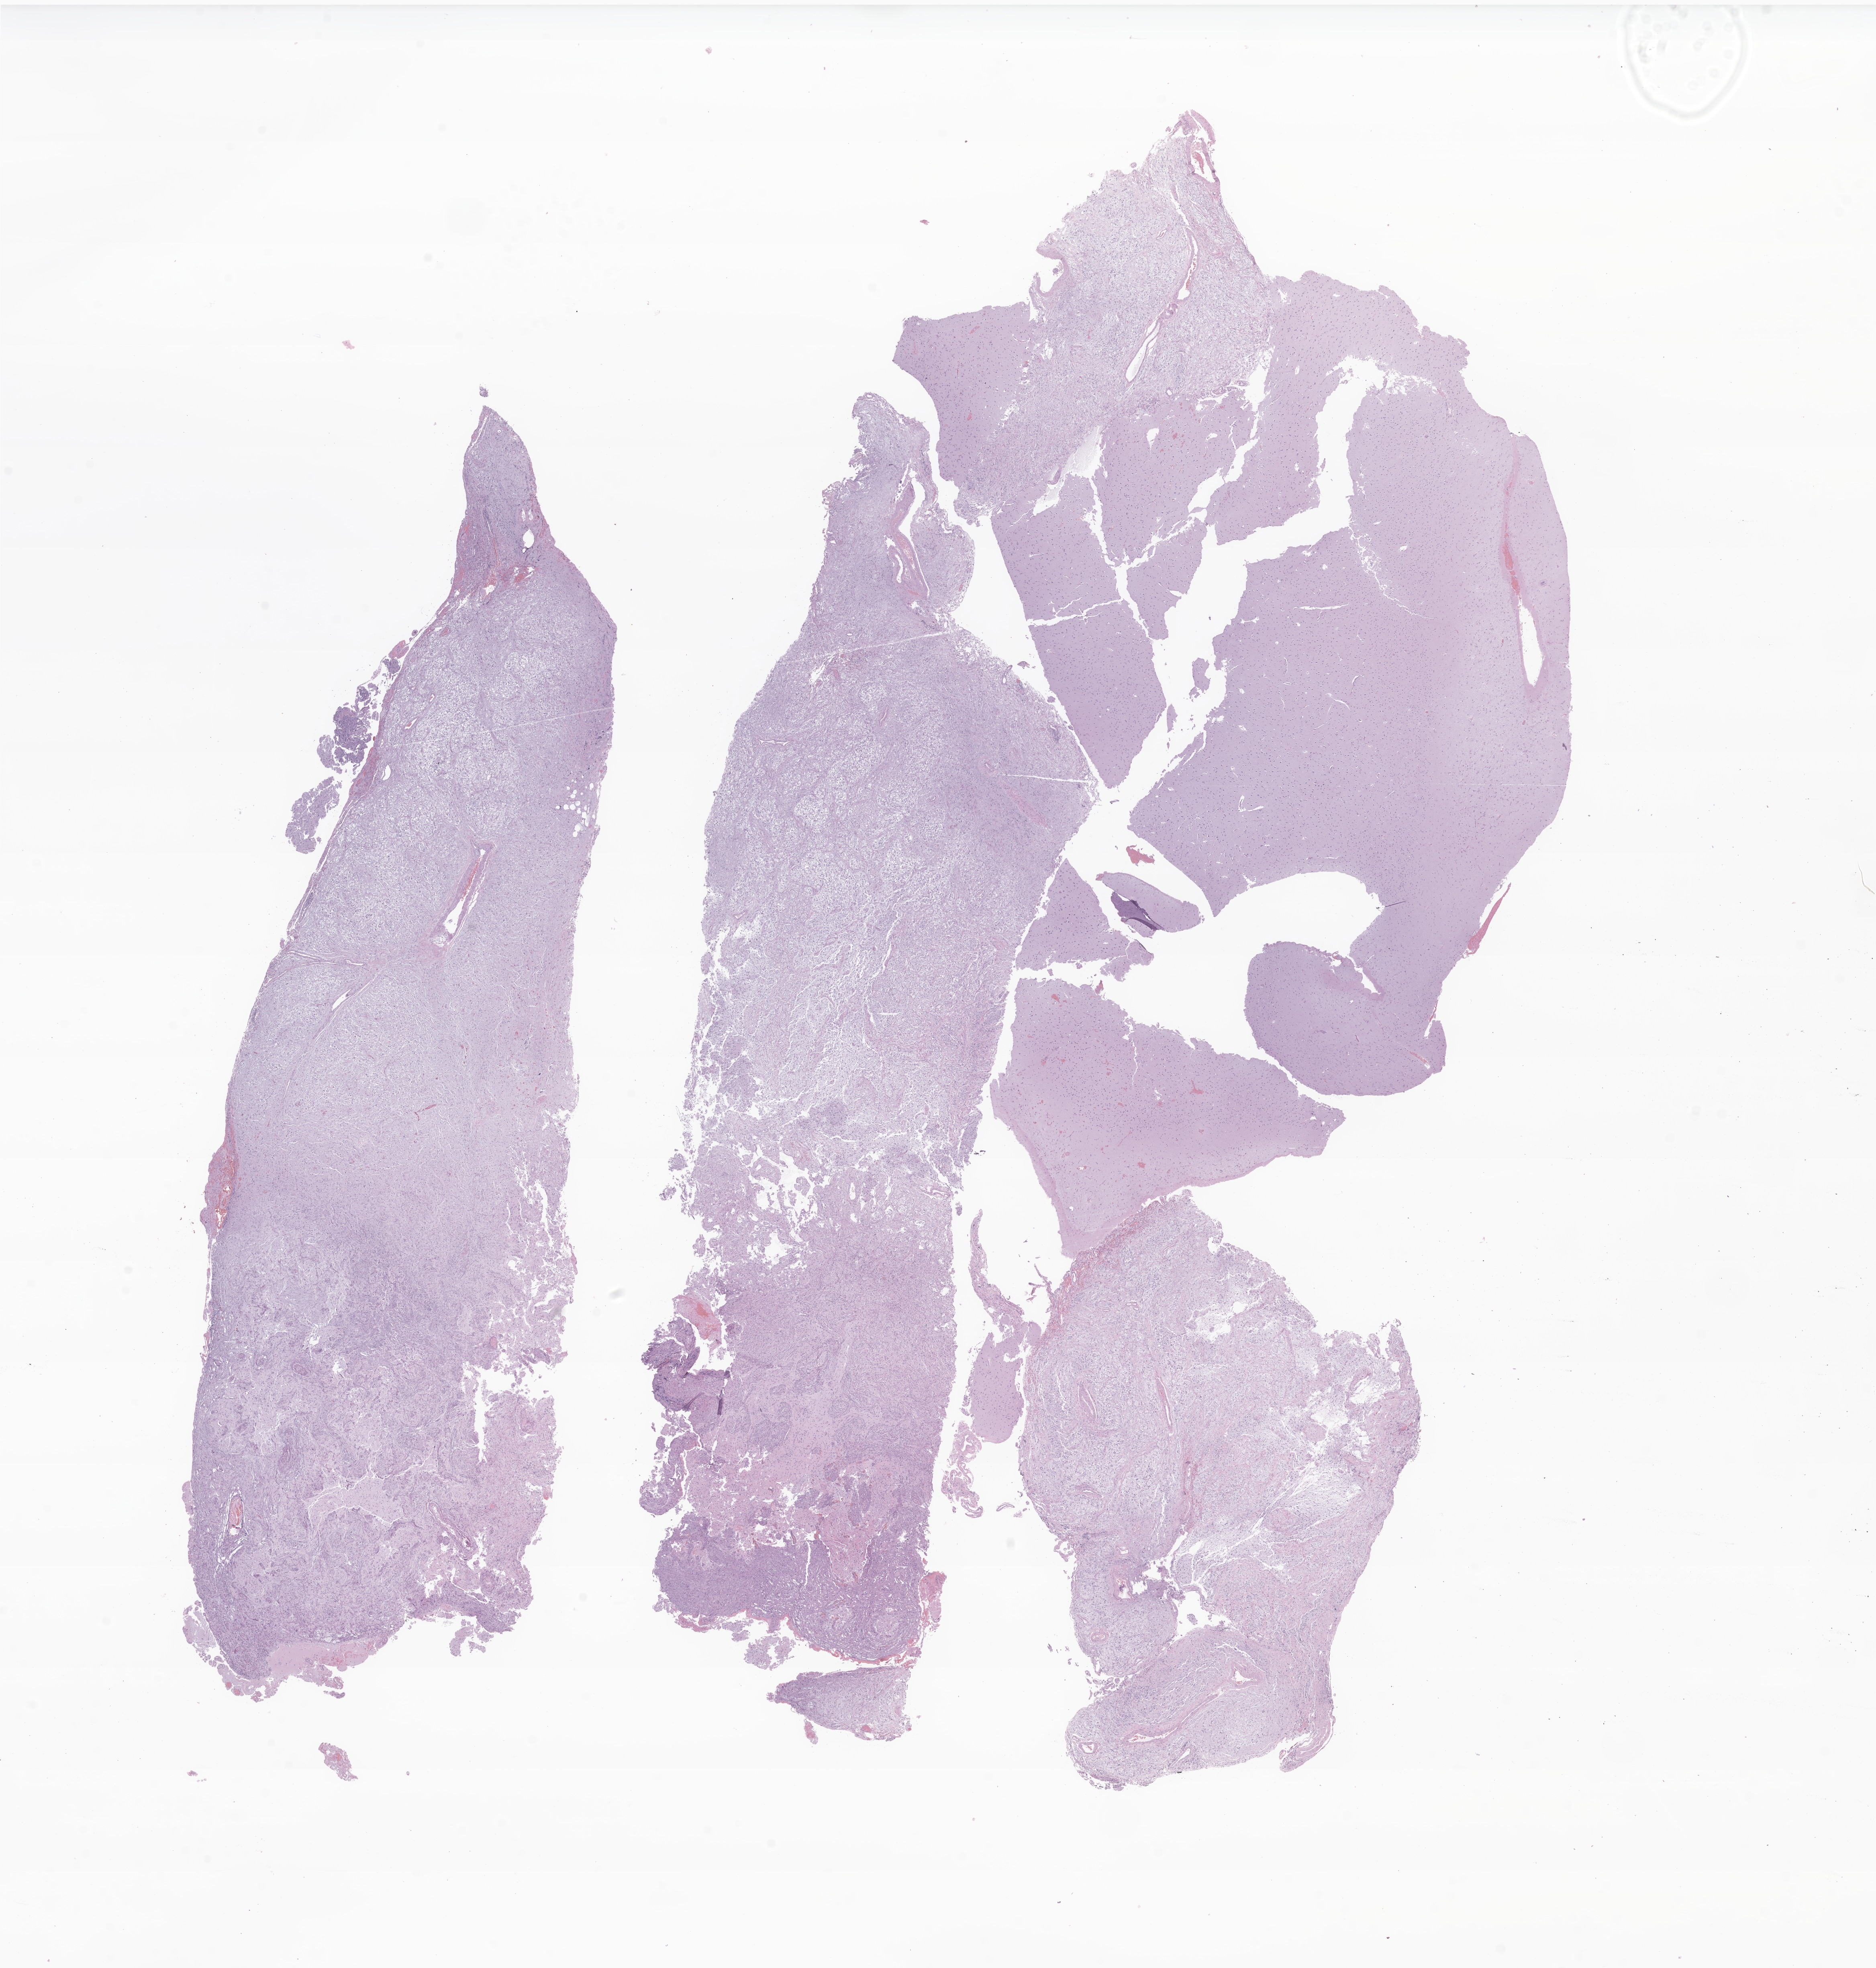
Whole-slide image, haematoxylin and eosin stain of tumor tissue from the brain, low-resolution overview of the scanned area, about 19.7 x 20.7 mm. Formalin-fixed paraffin-embedded section. Patient female; age 198 months (16 years 6 months).
• diagnosis: Ganglioglioma, NOS